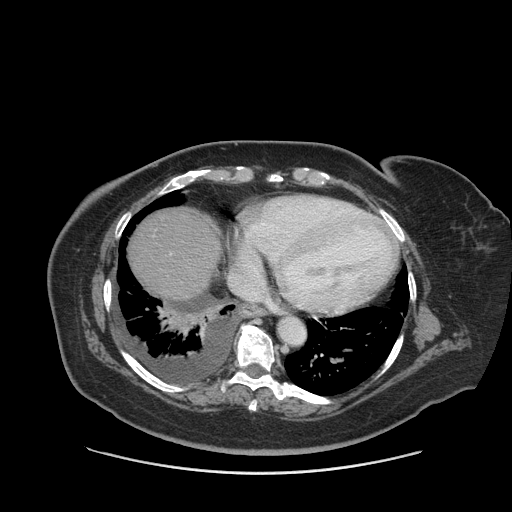
Contrast-enhanced abdominal CT (liver protocol), one axial slice; slice 80 of 91 in the series (ordered by position); reconstruction kernel STANDARD; 140 kVp; soft-tissue window (W 400 / L 40 HU); 2.5 mm slice thickness; 512 × 512 image matrix, field of view 420 × 420 mm. From the clinical record (not read from this slice): diagnosis: hepatocellular carcinoma (patient treated with transarterial chemoembolisation; whether this scan precedes or follows treatment is not stated here); TNM stage (as recorded): Stage-I; Child-Pugh class: A; tumour differentiation: well differentiated; tumour nodularity: uninodular.
Outlined on this slice (semi-automatically segmented with operator editing):
- abdominal aorta: box from (x=279, y=318) to (x=305, y=345) px
- liver parenchyma outside the tumour (the mass and vessels are separate outlines, so this box may not span the whole liver): (x=128, y=208)–(x=220, y=300)